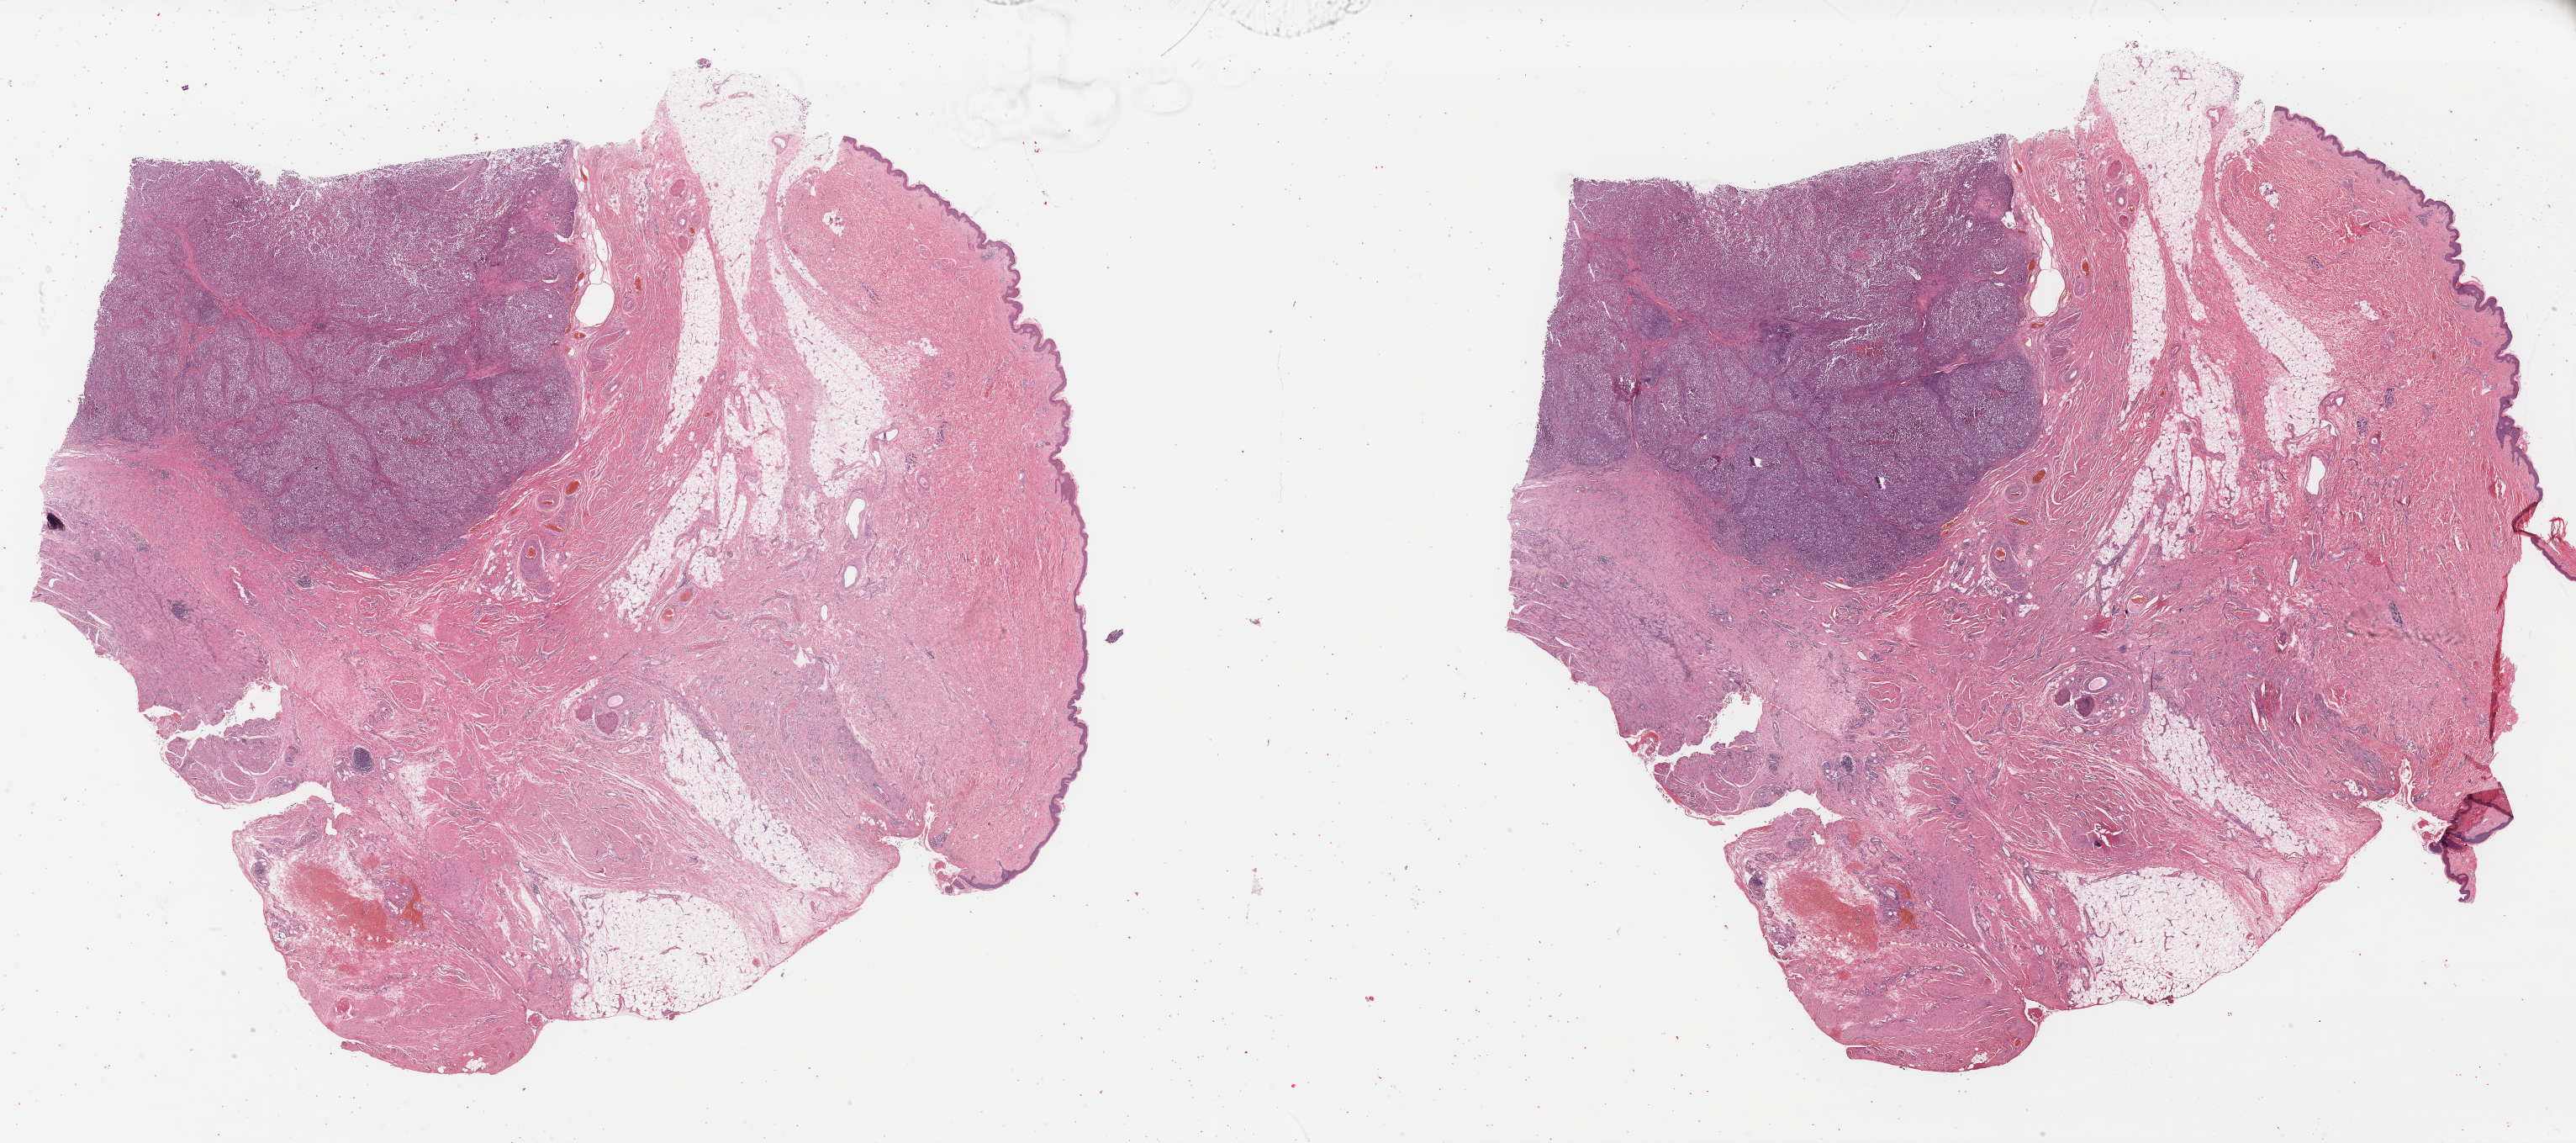
H&E whole-slide image — whole scanned area (about 48.2 x 21.4 mm) shown as a low-resolution overview, formalin-fixed paraffin-embedded (FFPE) diagnostic section, metastatic tumour sample, sampled site: lymph node. Patient: male, age at initial diagnosis 74 years.
• this section: metastatic tumour tissue
• patient diagnosis: Malignant melanoma, NOS